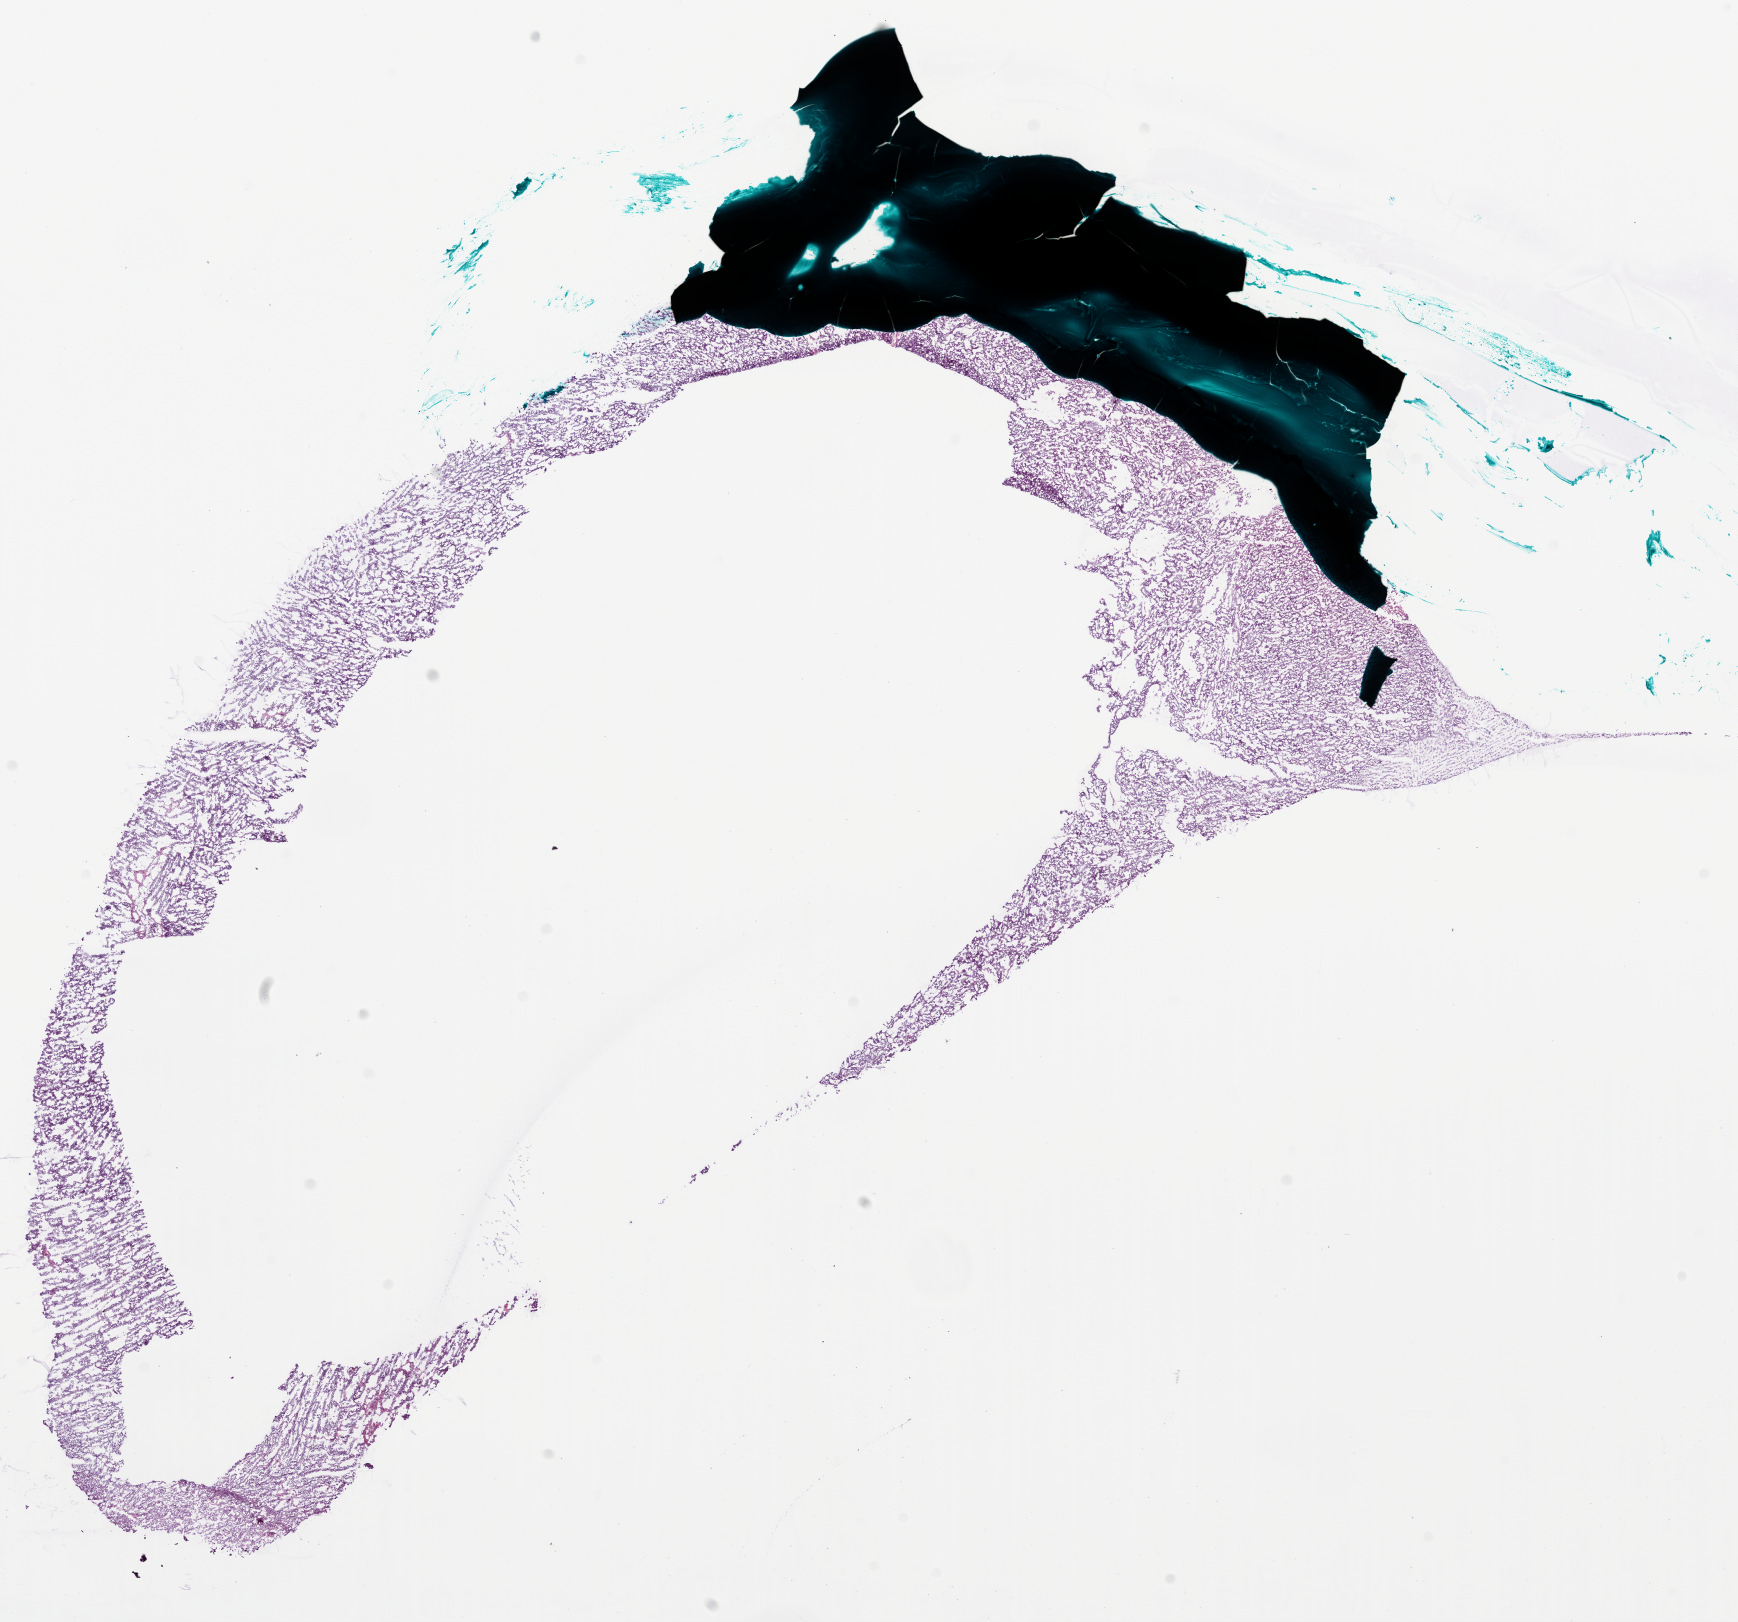
Whole-slide histology image, Hematoxylin and eosin (H&E) stained, shown as a low-resolution overview of the whole scanned area (about 14.0 x 13.1 mm, acquisition: 20x scan); frozen section from the bottom of the tissue portion; ovary, primary tumour sample. Female patient; age at initial diagnosis 50 years. Histologic grade: G3 (poorly differentiated). Slide review estimates, as recorded: tumour cells 98%, tumour nuclei 99%, normal cells 1%, necrosis 1%.
FIGO stage: IIIC. Pathologic diagnosis: Serous cystadenocarcinoma, NOS.